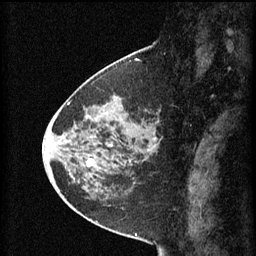
Breast MRI (dynamic contrast-enhanced), one sagittal slice. Slice 28 of 60 in the series (ordered by position). 3 images stored at this slice position (order not interpretable as contrast timing). 1.5 T. TE 4.2 ms, TR 8.2 ms. 256 × 256 image matrix, field of view 200 × 200 mm. Patient: female, 45 years.
Structures marked on this image (semi-automatic segmentation, software-assisted and operator-edited):
- analysis volume of interest (the breast-tissue region the enhancement analysis was run in; not a lesion): bounding box <80,102,157,171> (left, top, right, bottom; pixels)
- tumour enhancement mask (voxels above the 70 % enhancement threshold inside the analysis volume of interest): <87,160,94,167>